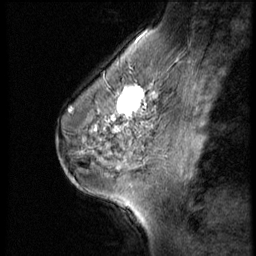
Breast MRI (dynamic contrast-enhanced), one sagittal slice. Slice 38 of 56 in the series (ordered by position). 3 images stored at this slice position (order not interpretable as contrast timing). 1.5 T. TE 4.2 ms, TR 9 ms. 256 × 256 image matrix, field of view 180 × 180 mm. Patient: female, 45 years. Case-level facts recorded for this patient, not image findings: setting: breast cancer imaged before/during neoadjuvant chemotherapy; receptor status: HR-positive, HER2-negative.
Outlined on this slice (semi-automatic segmentation, software-assisted and operator-edited):
- analysis volume of interest (the breast-tissue region the enhancement analysis was run in; not a lesion): bounding box <102,77,166,129> (left, top, right, bottom; pixels)
- tumour enhancement mask (voxels above the 140 % enhancement threshold inside the analysis volume of interest): <102,77,159,129>